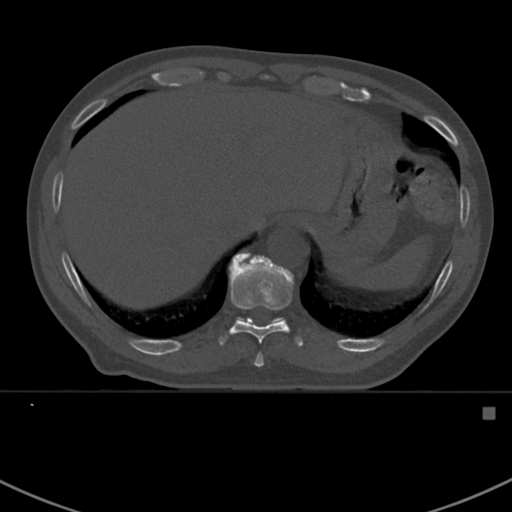
CT including the spine, one axial slice. Position 364 of 412 along the scan axis. 120 kVp. Bone window (W 1800 / L 400 HU). 1.5 mm slice thickness. 512 × 512 image matrix, field of view 358 × 358 mm. Male patient, age 59 years. From the clinical record (not read from this slice): primary cancer: prostate.
Outlined on this slice (semi-automatically segmented with operator editing):
- T10 vertebra: box from (x=219, y=253) to (x=303, y=367) px
- T11 vertebra: (x=238, y=253)–(x=285, y=322)
- T9 vertebra: (x=255, y=353)–(x=262, y=361)